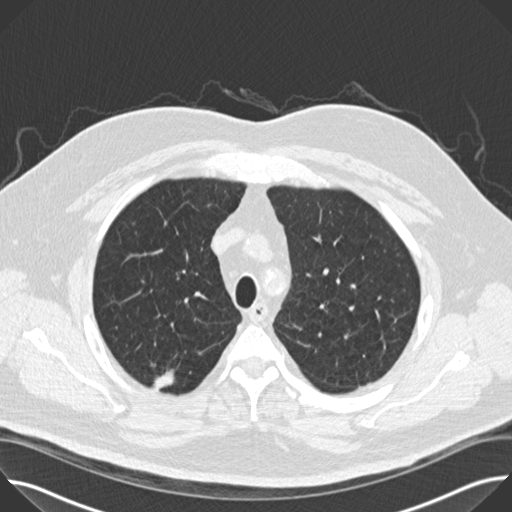
Axial slice from a low-dose chest CT screening exam. Baseline annual screen. Lung window (W 1500 / L -600 HU). 2 mm slice thickness. Standard (soft-tissue) reconstruction kernel (B30f). Male participant, aged 65 years at enrolment.
Expert-annotated lung lesion, bounding box (x1, y1, x2, y2) in pixels: (148, 359, 191, 416). The screening reader recorded 2 non-calcified nodules or masses ≥4 mm on this exam (right upper lobe, right upper lobe); which of them this box marks is not recorded. Participant outcome: lung cancer diagnosed 47 days after this screen — bronchiolo-alveolar adenocarcinoma, NOS, right upper lobe, moderately differentiated (G2), stage IIA (AJCC 6th edition), 14 mm at pathology.